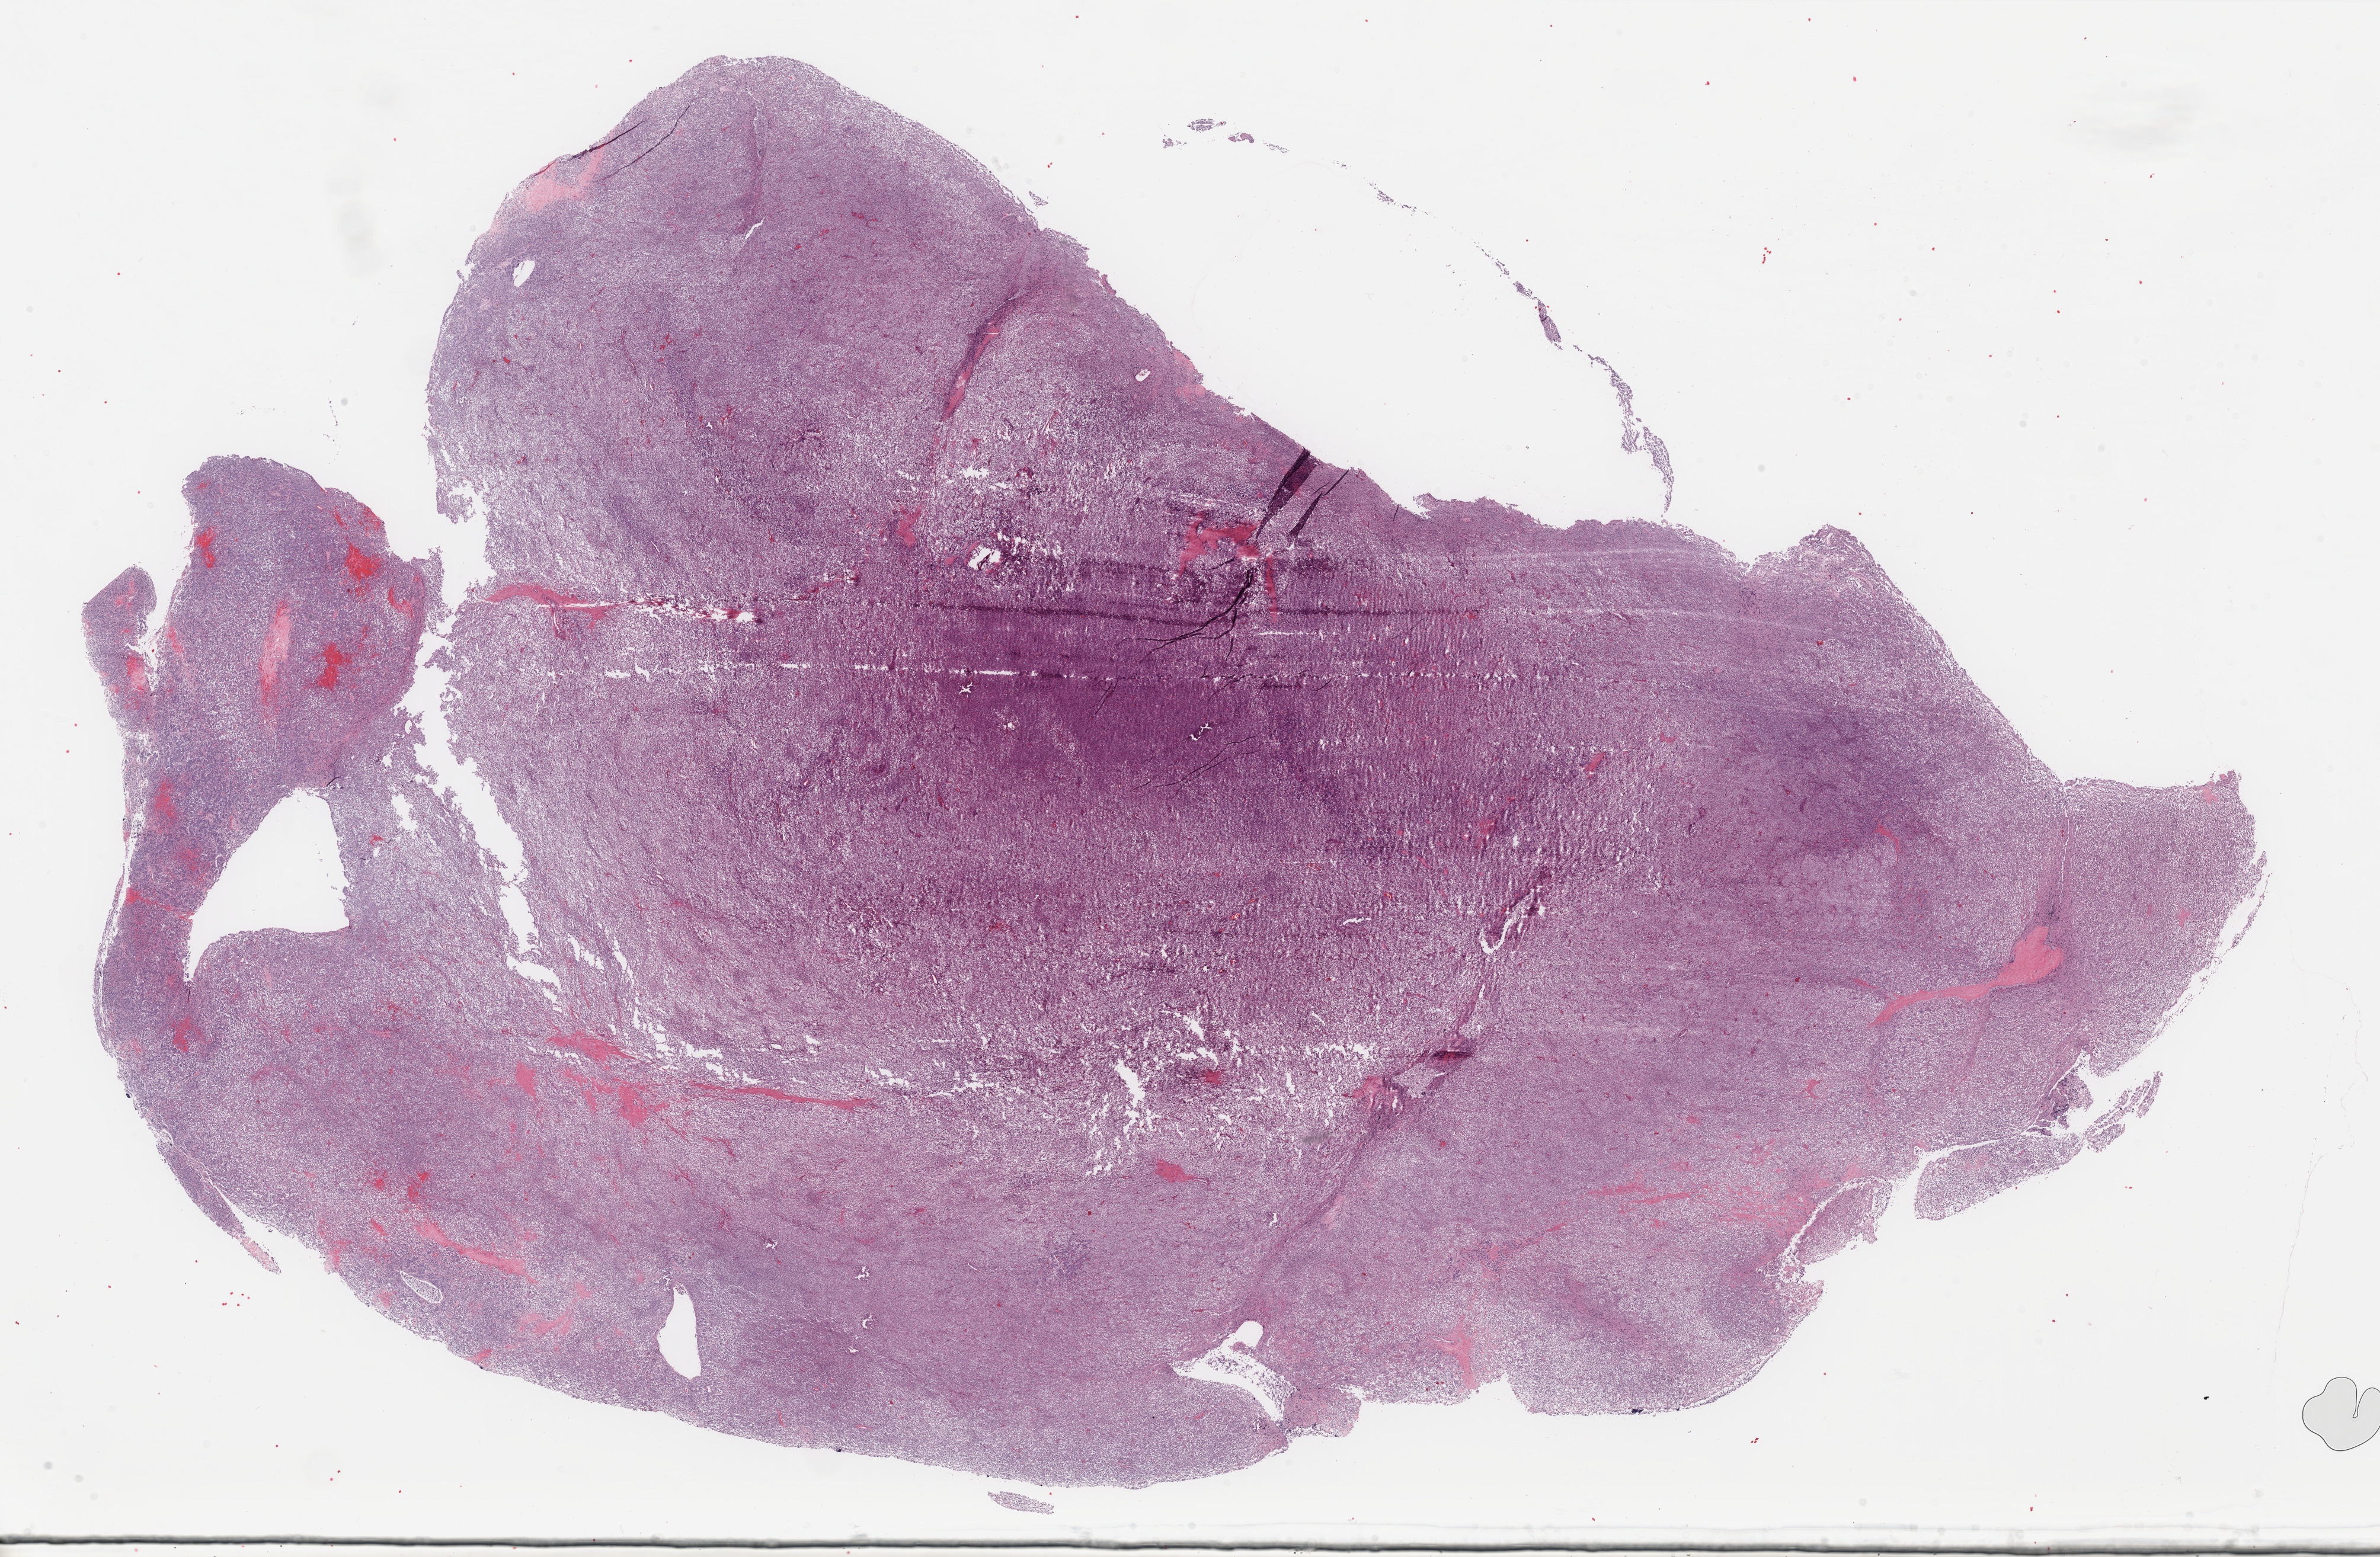
Whole-slide histology image, Hematoxylin and eosin (H&E) stained — a low-resolution overview of the entire scanned area, about 31.8 x 20.8 mm (acquisition: 40x scan), formalin-fixed paraffin-embedded (FFPE) diagnostic section, adrenal gland, primary tumour sample. Patient: female, age at initial diagnosis 42 years.
* laterality: left
* pathologic diagnosis: Pheochromocytoma, malignant
* lymph nodes positive (case pathology): 13 of 15 examined